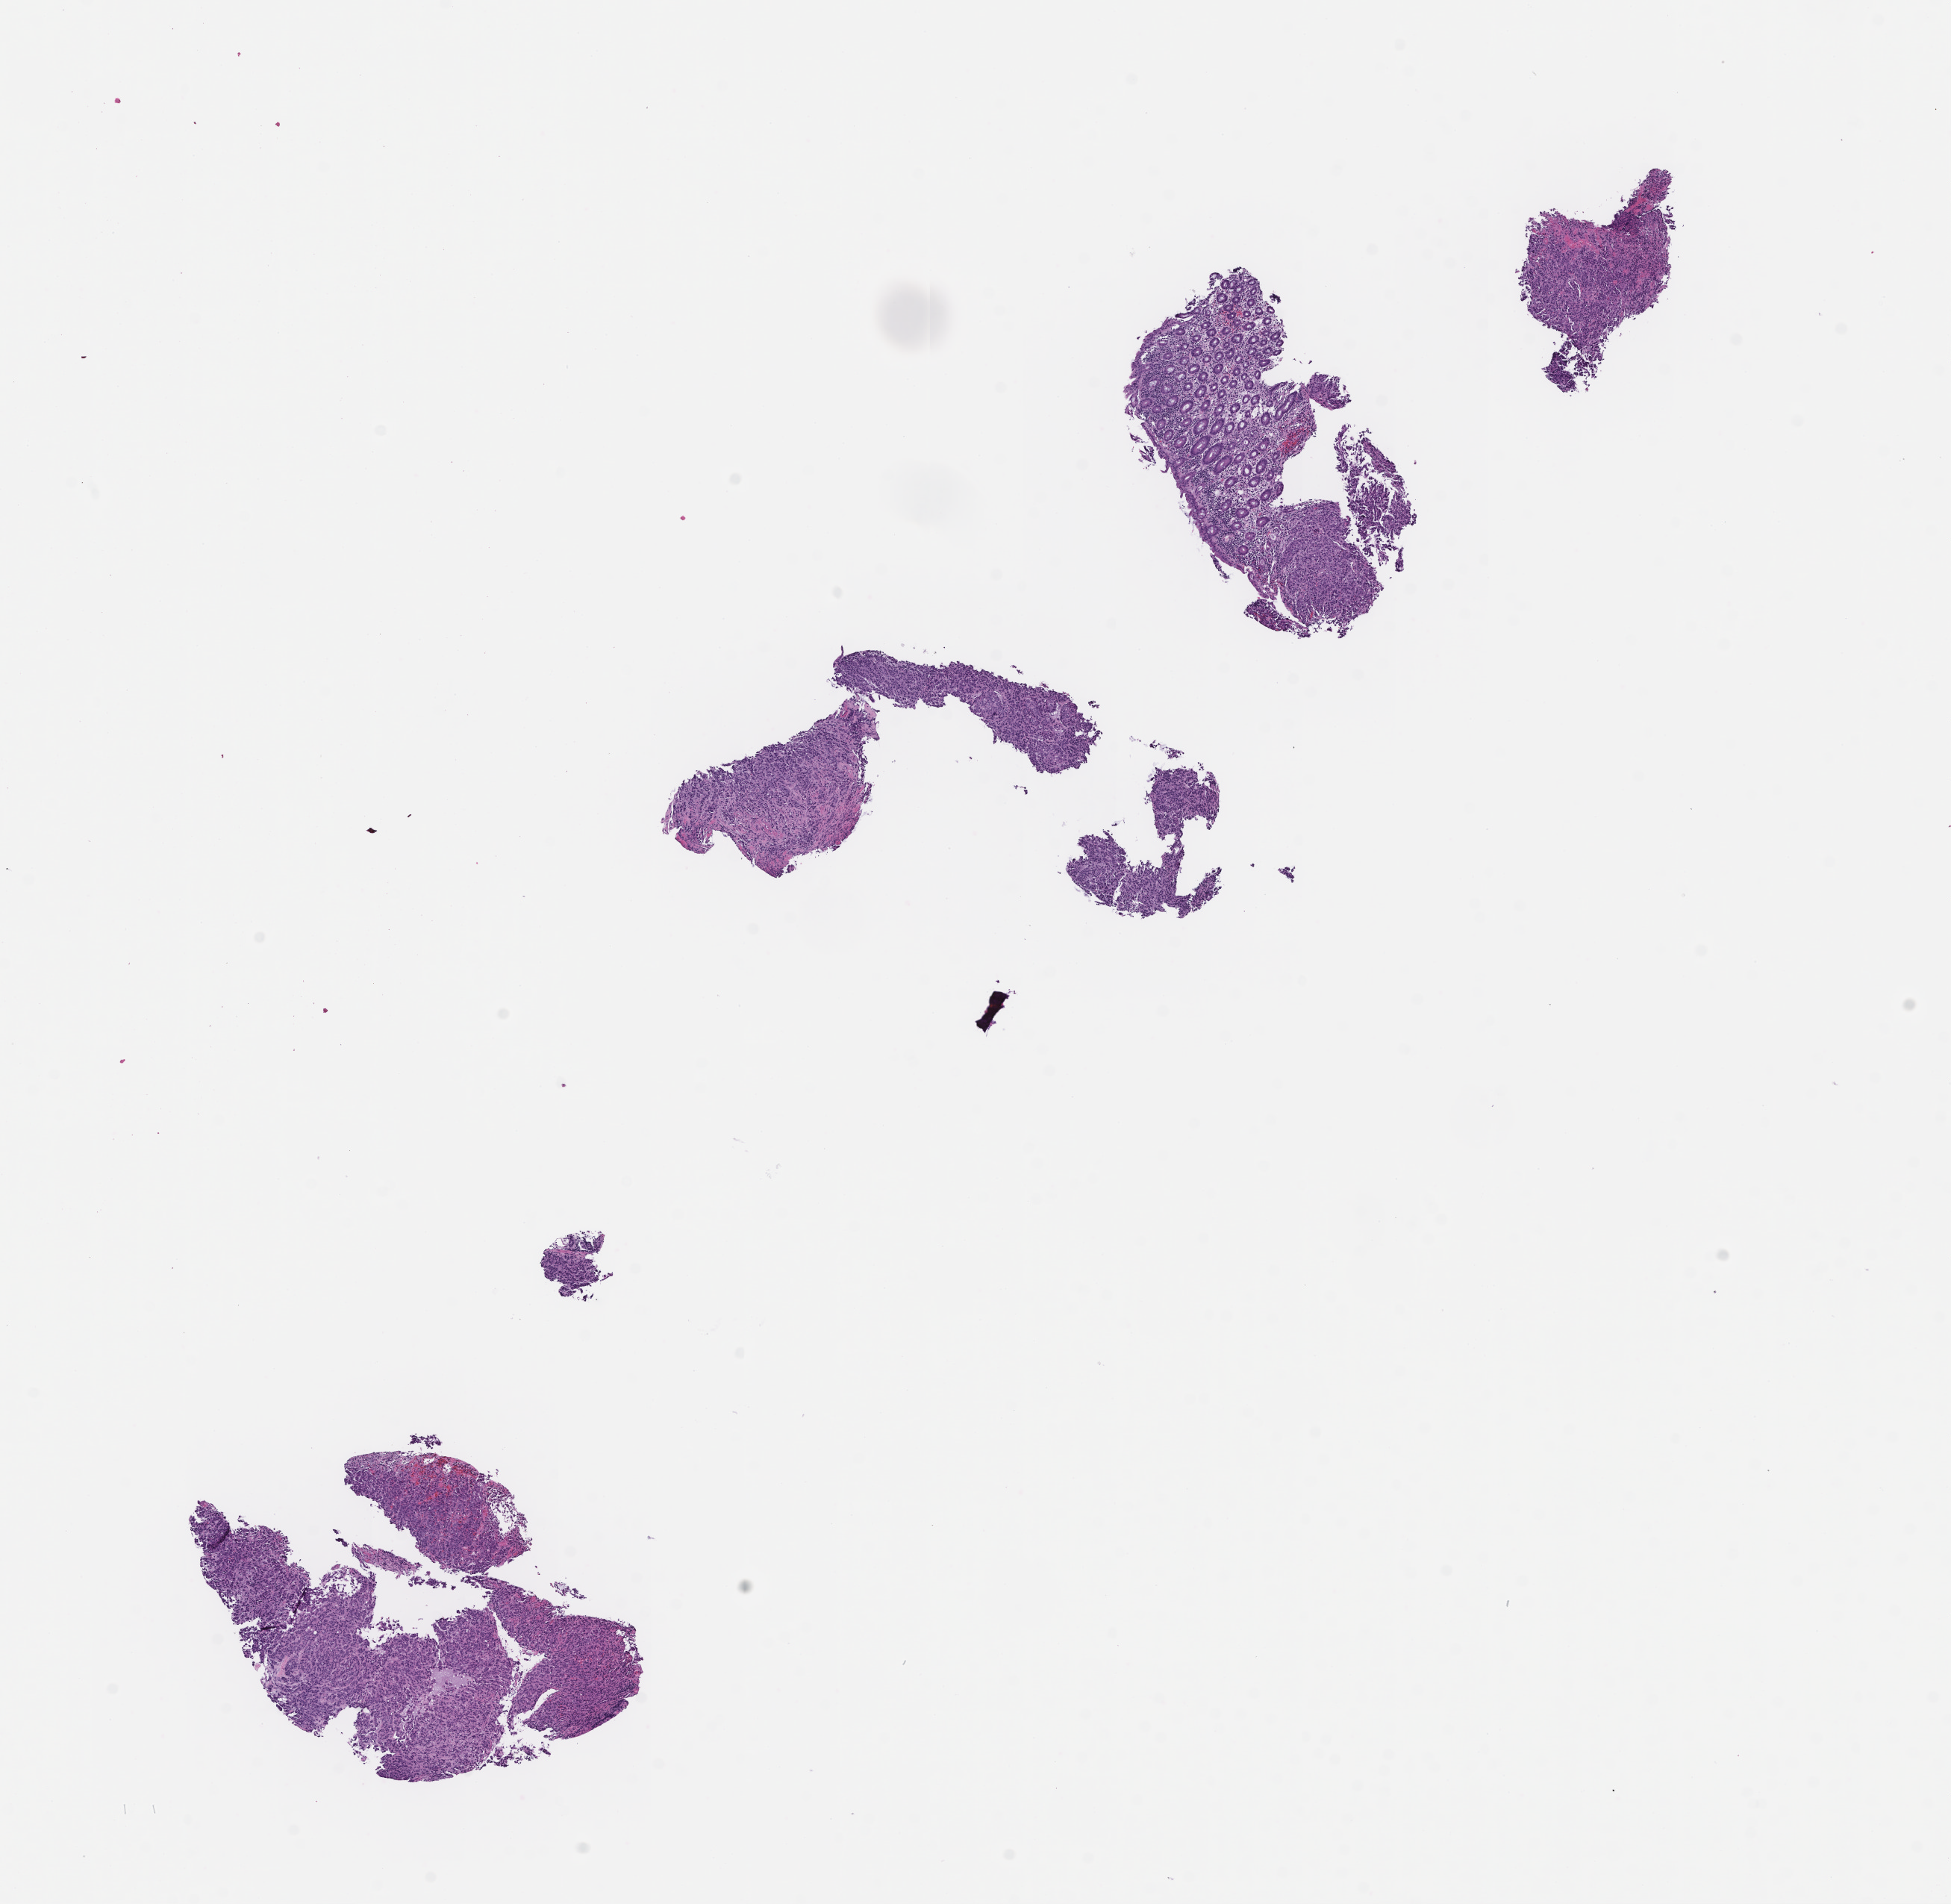
Digitized H&E-stained section, low-resolution overview of the scanned area, about 10.6 x 10.3 mm; formalin-fixed, paraffin-embedded (FFPE) tissue; tissue site: colon; archival tissue. Patient: female.
This section: primary tumour tissue. Diagnosis: Colorectal Carcinoma.